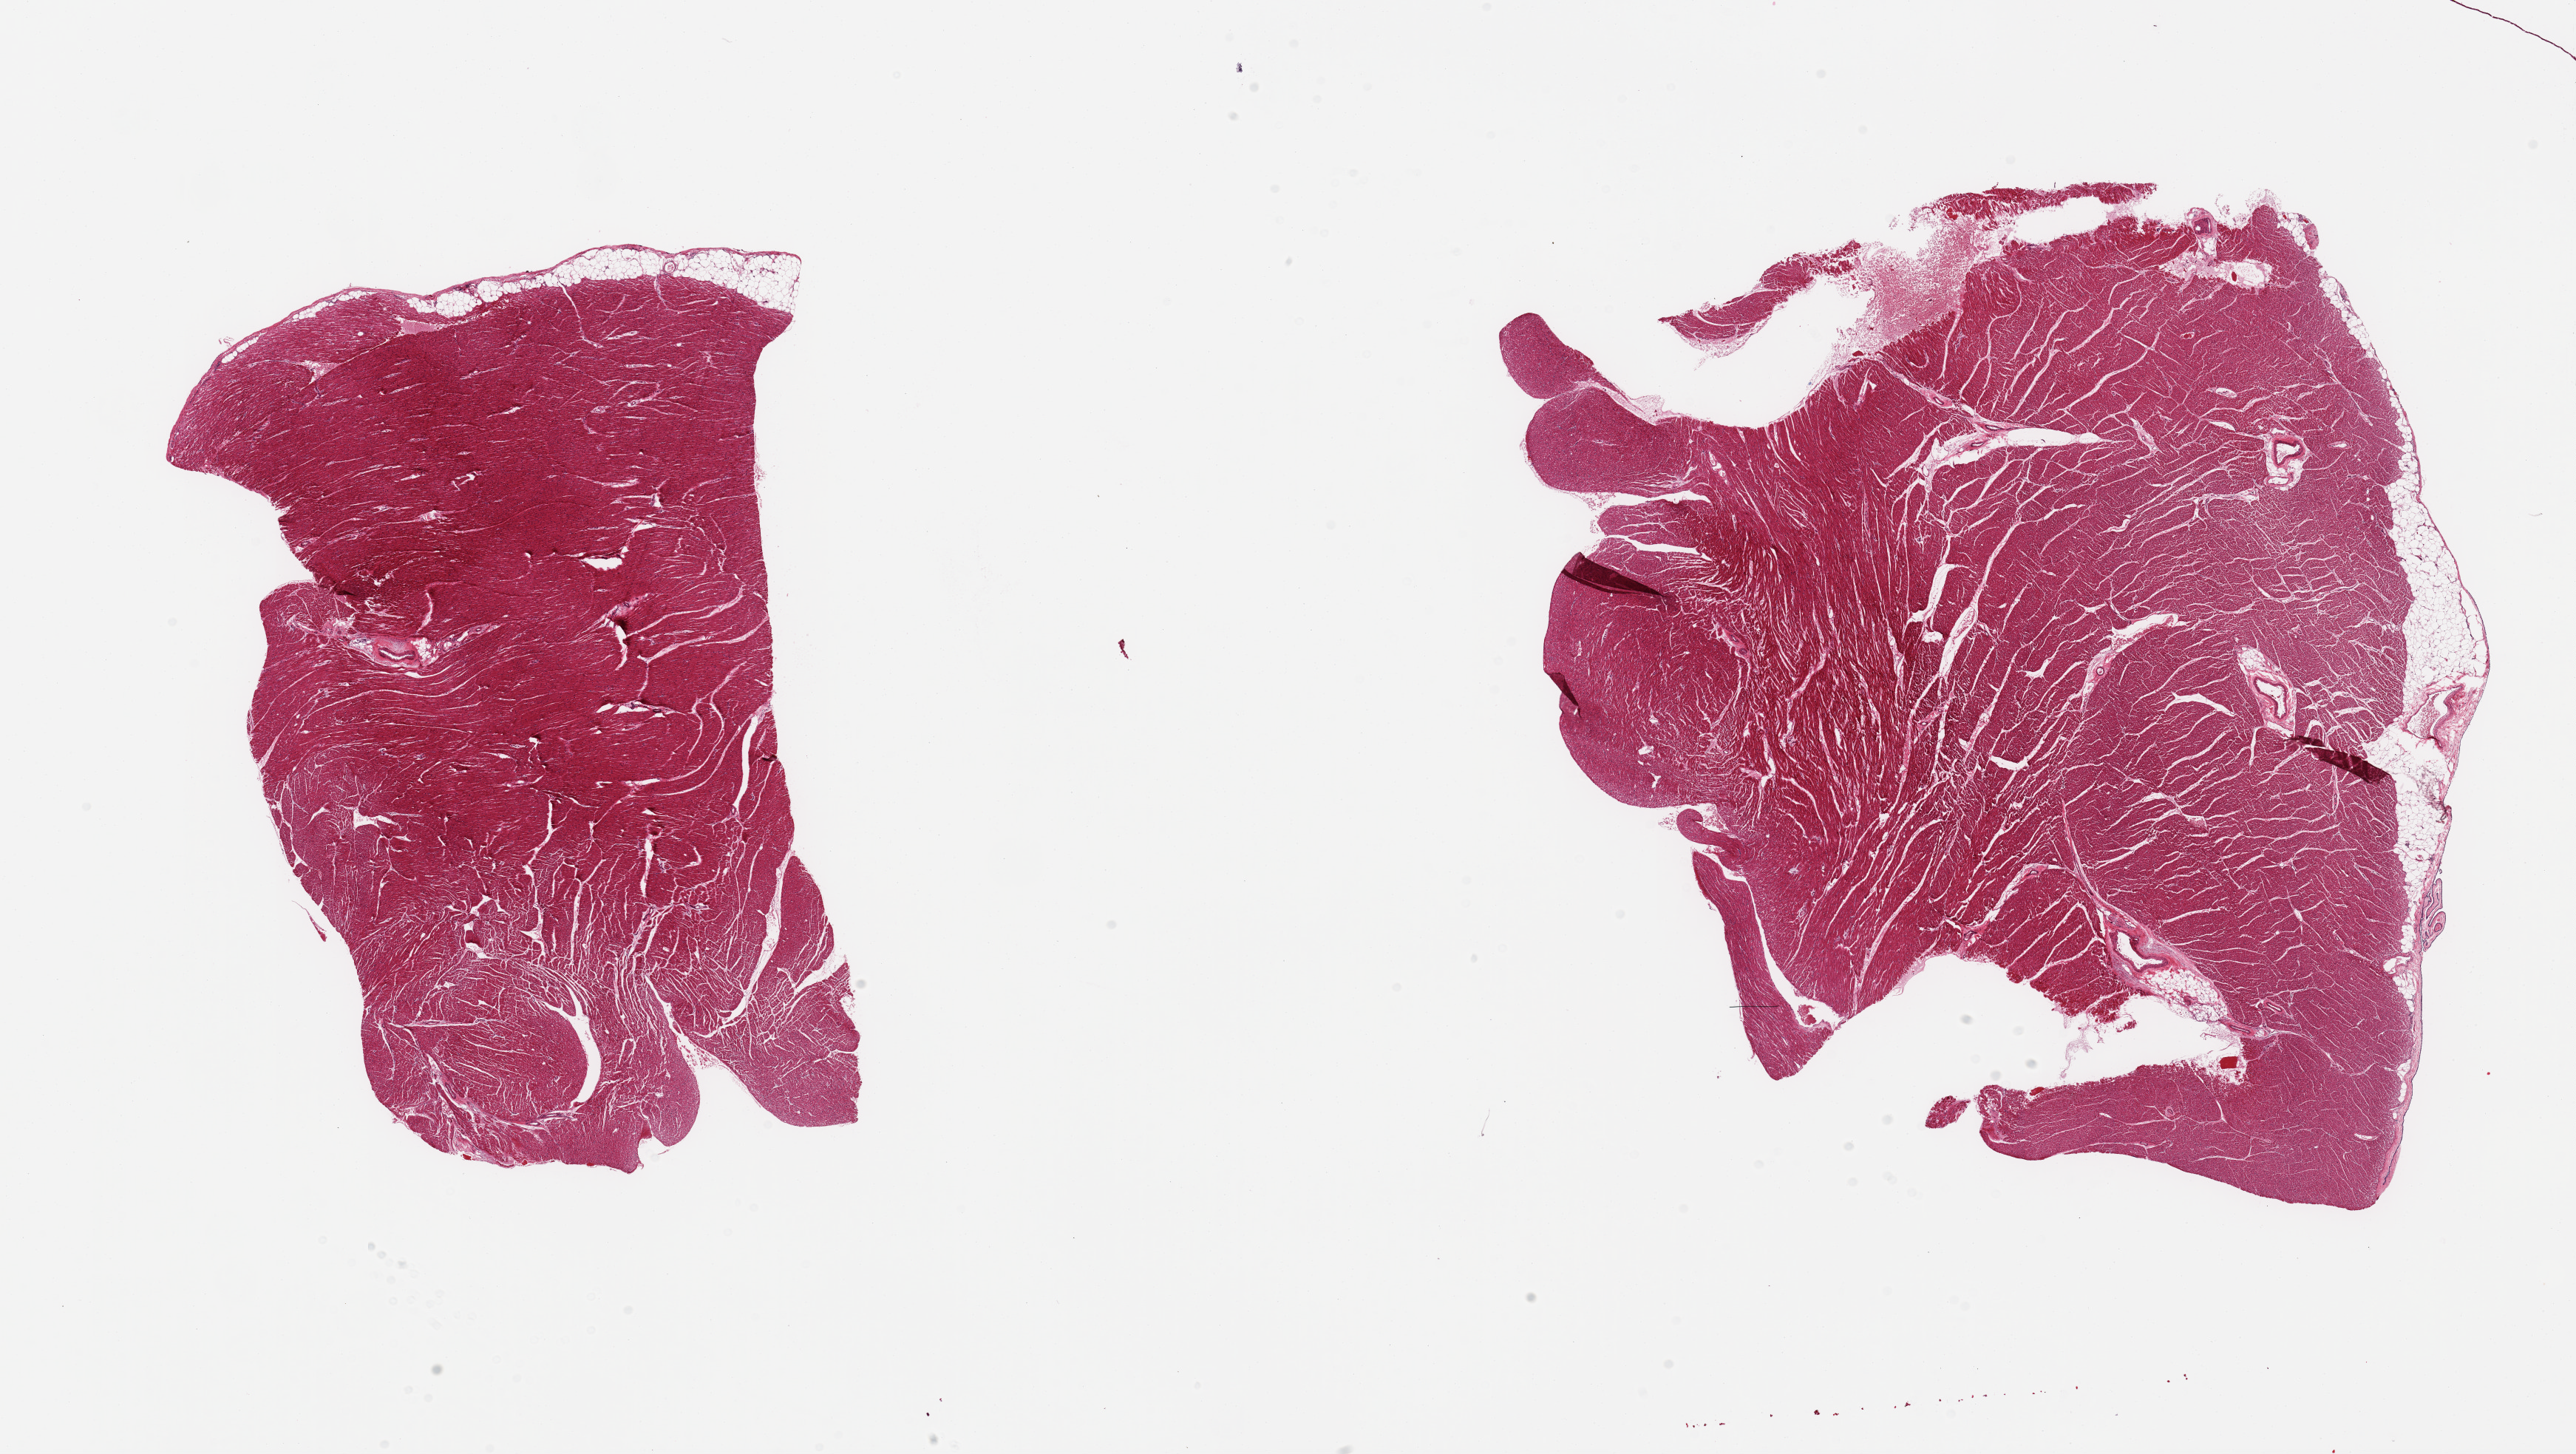
Hematoxylin and eosin (H&E) whole-slide image, brightfield — a low-resolution overview of the entire scanned area, about 27.6 x 15.6 mm; PAXgene-fixed, paraffin-embedded tissue; sampled site (target tissue): heart; donor tissue sample. Donor: female.
Review note (as recorded): 2 pieces.